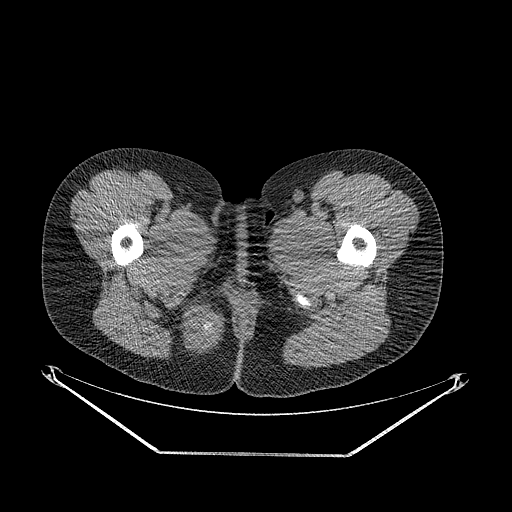
CT of an extremity soft-tissue mass (from a PET/CT study), one axial slice; position 29 of 267 along the scan axis; soft-tissue window (W 400 / L 40 HU); 3.75 mm slice thickness; 512 × 512 image matrix. Female patient. Case-level facts recorded for this patient, not image findings: histological type: epithelioid sarcoma; grade: intermediate; site of the primary tumour: right buttock.
Outlined on this slice (expert contour drawn on MRI and transferred to this co-registered scan by the dataset authors):
- gross tumour volume including surrounding oedema: box from (x=173, y=297) to (x=225, y=359) px
- gross tumour volume (mass): (x=178, y=306)–(x=223, y=352)